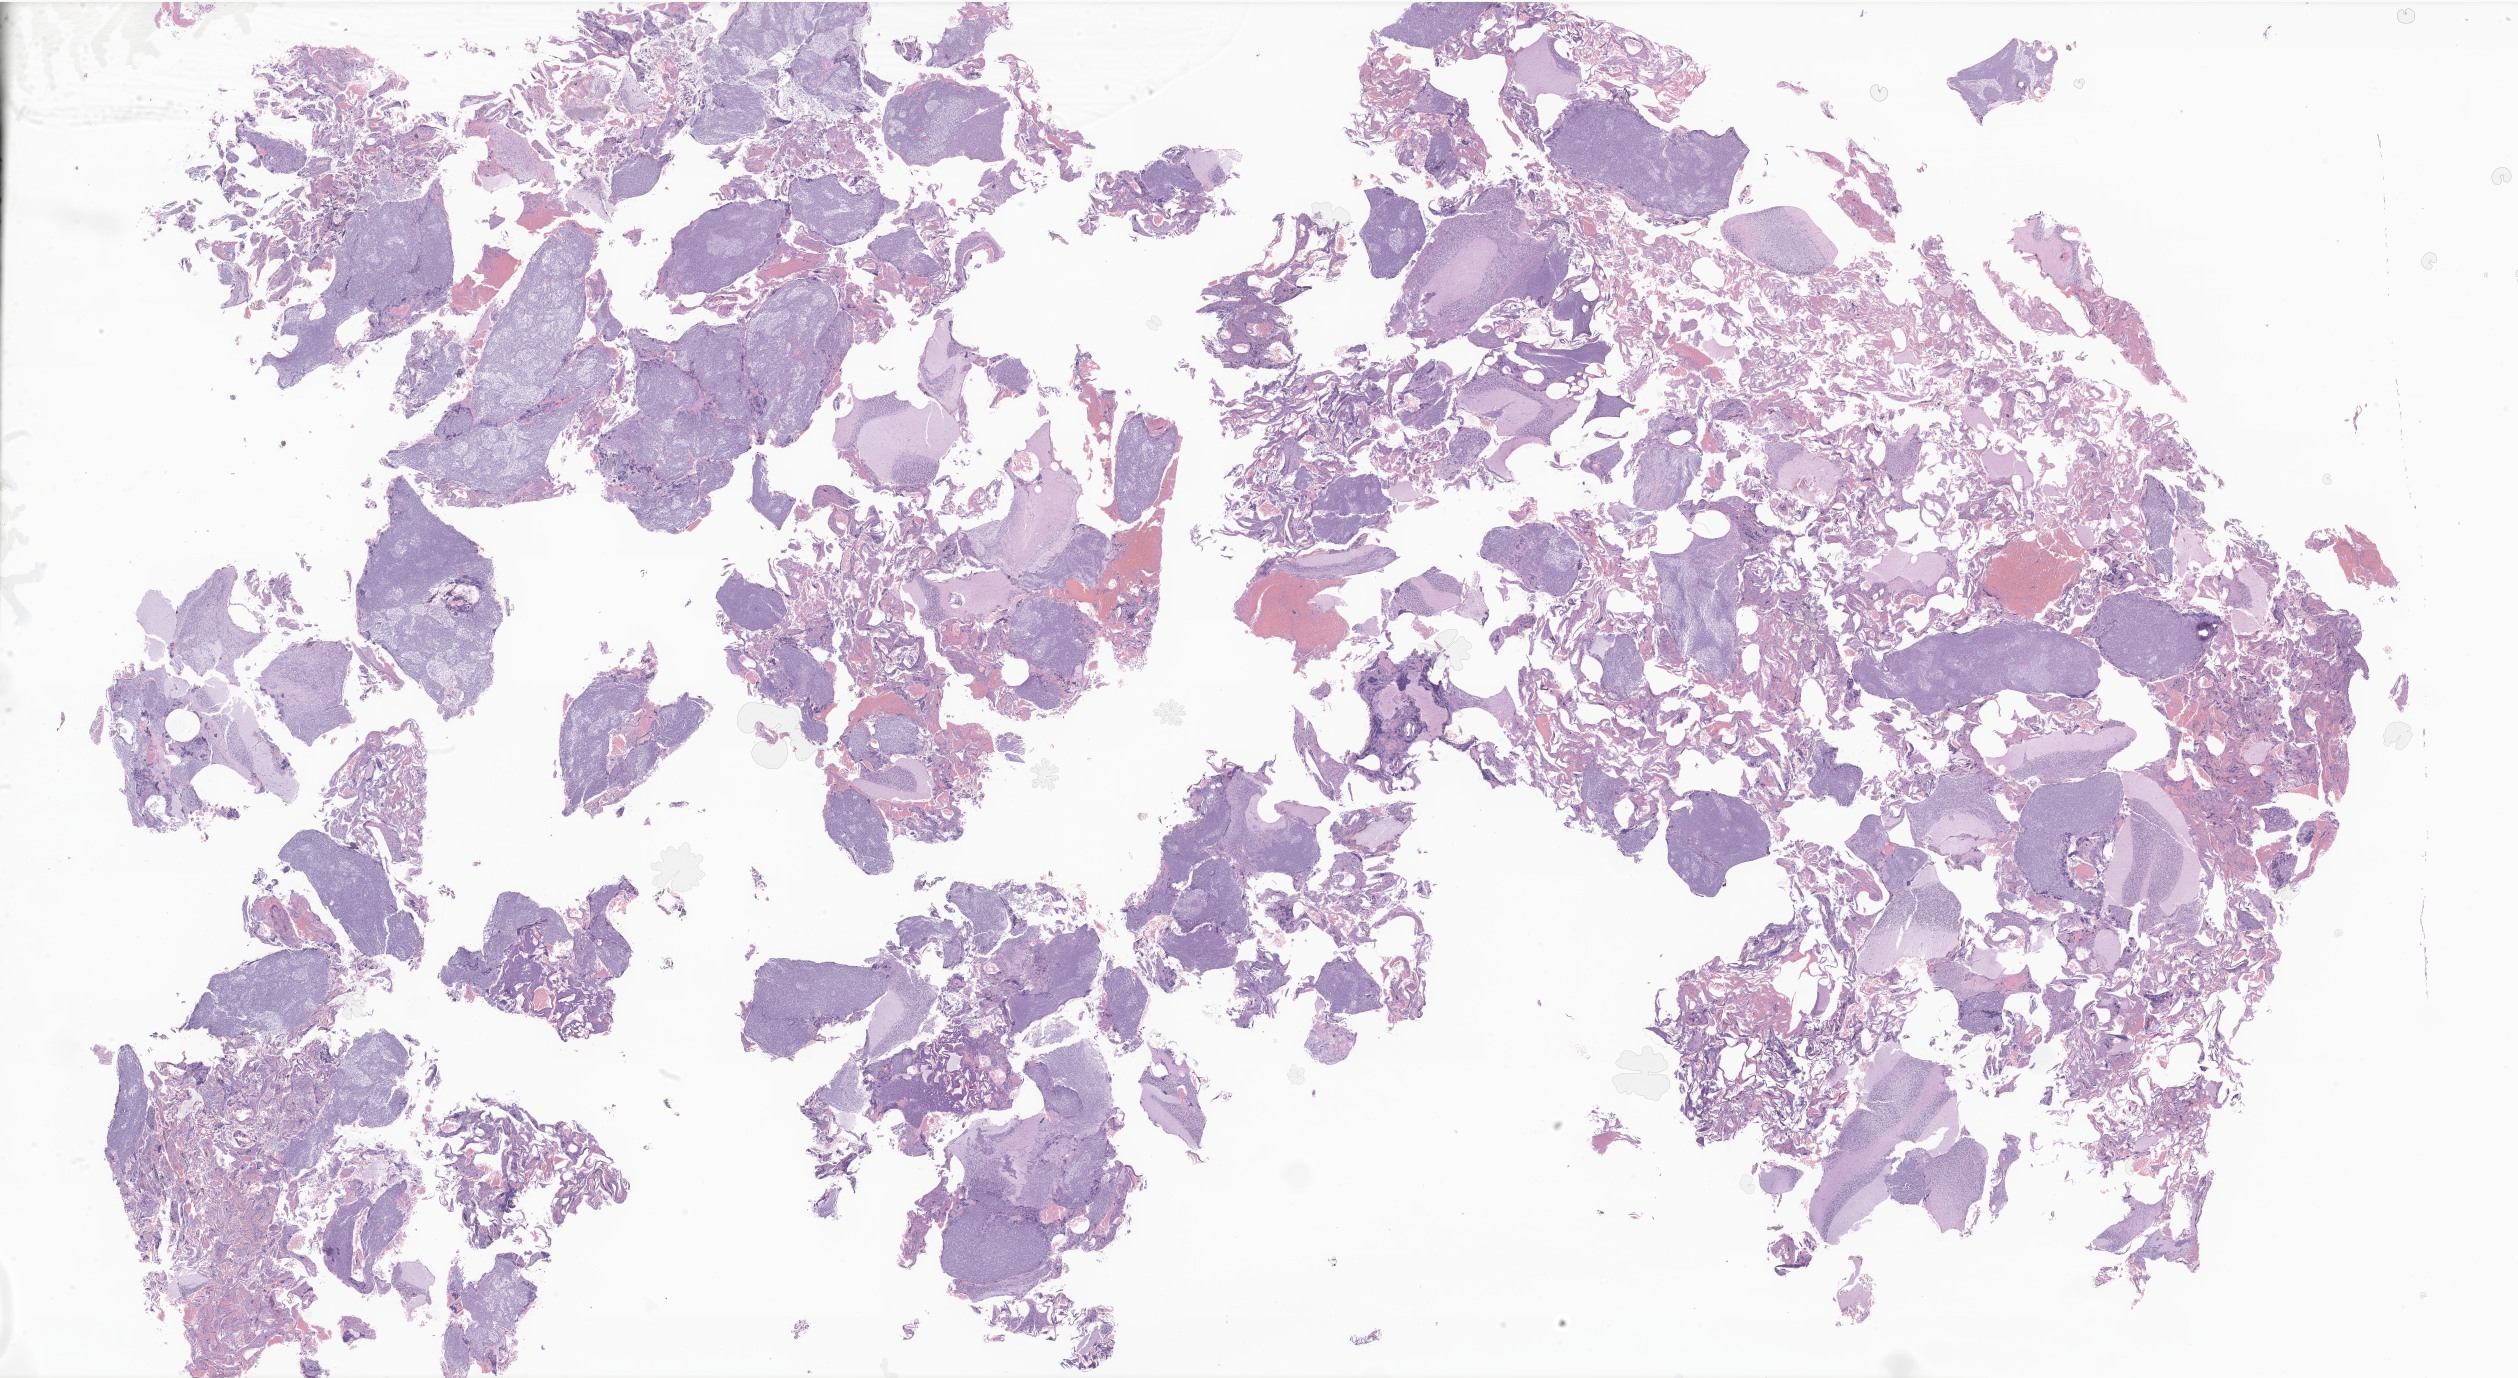
H&E whole-slide image of tumor tissue from the cerebellum — low-resolution overview of the scanned area, about 42.5 x 23.2 mm, FFPE section. Patient: male, age 201 months (16 years 9 months).
* diagnosis (ICD-O-3 morphology term): Medulloblastoma, NOS